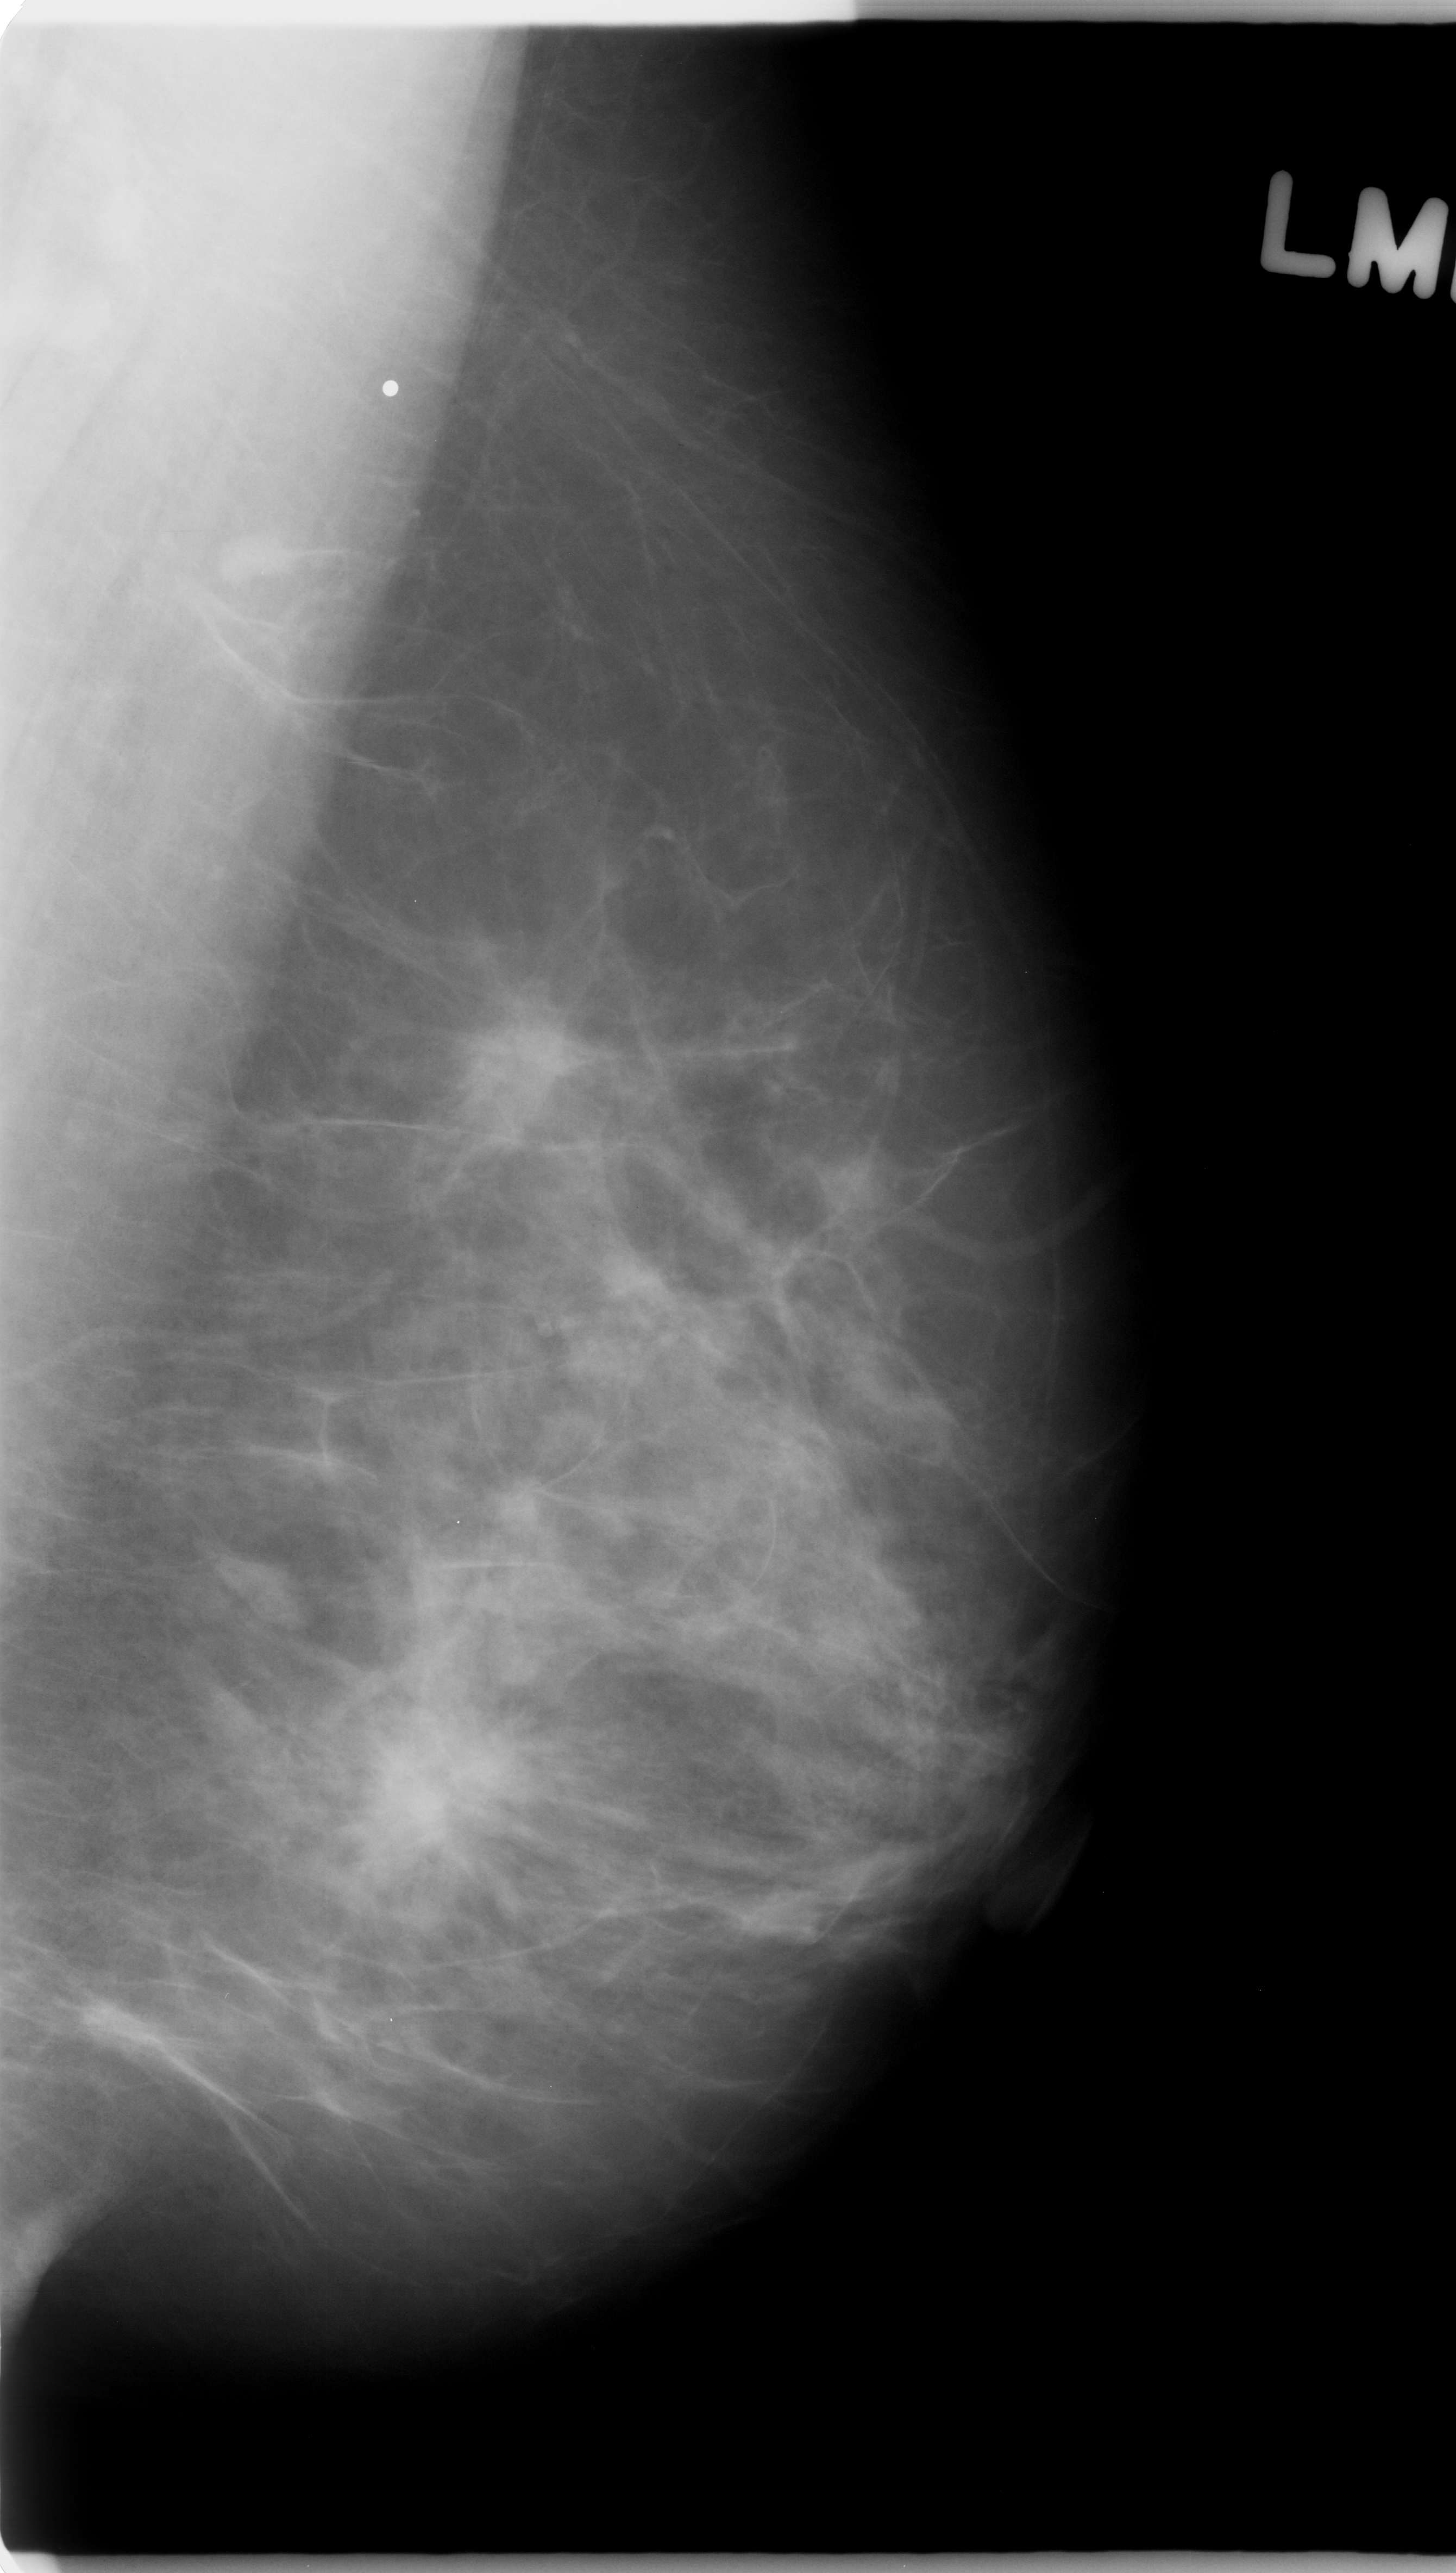
Digitized screen-film mammogram; left breast; MLO view; BI-RADS breast density category 2 (scale 1–4).
- Radiologist-marked abnormalities on this image: Finding 1 of 2: mass, shape architectural distortion, margins spiculated; BI-RADS assessment category 5; subtlety rating 5 on a 1 (subtle) to 5 (obvious) scale; pathology result (as recorded, not read from the image): malignant.
- Finding 2 of 2: mass, shape architectural distortion, margins spiculated; BI-RADS assessment category 5; subtlety rating 5 on a 1 (subtle) to 5 (obvious) scale; pathology result (as recorded, not read from the image): malignant.